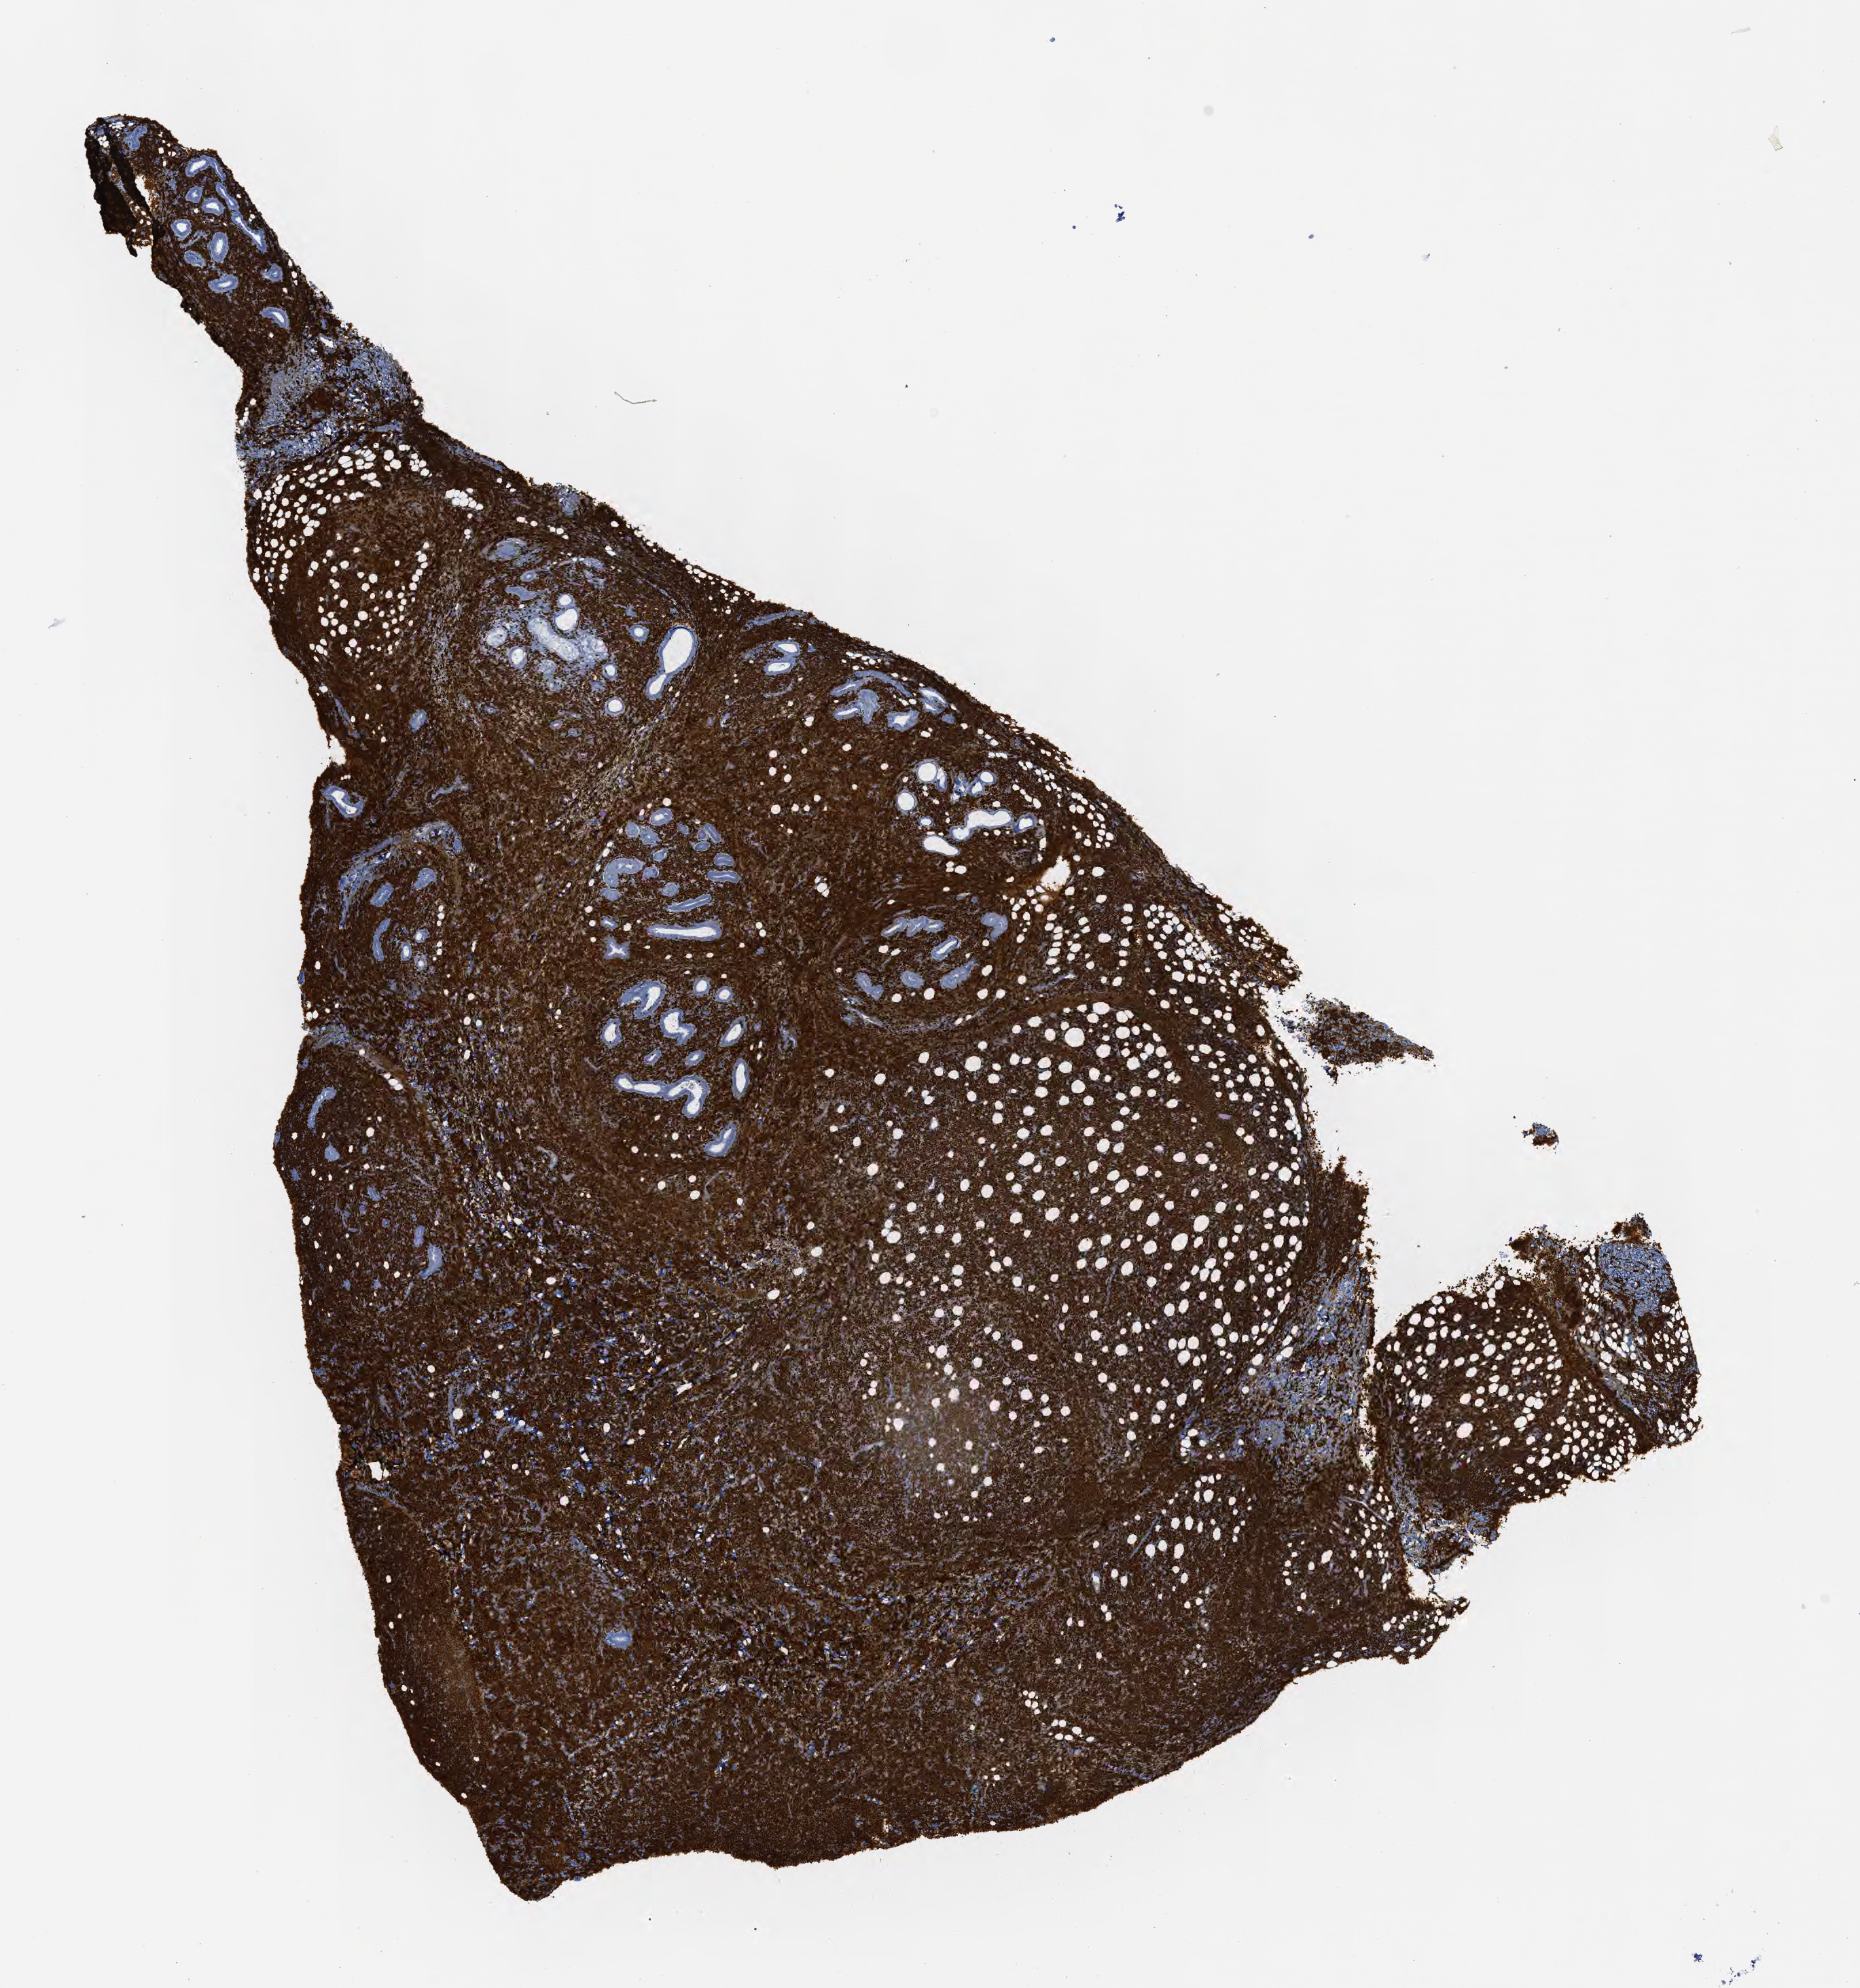
Whole-slide image, immunohistochemical stain for Ki-67, shown as a low-resolution overview of the whole scanned area (about 11.1 x 11.8 mm), specimen: tumor tissue. Male patient, 46 years old.
• diagnosis: Burkitt lymphoma, NOS